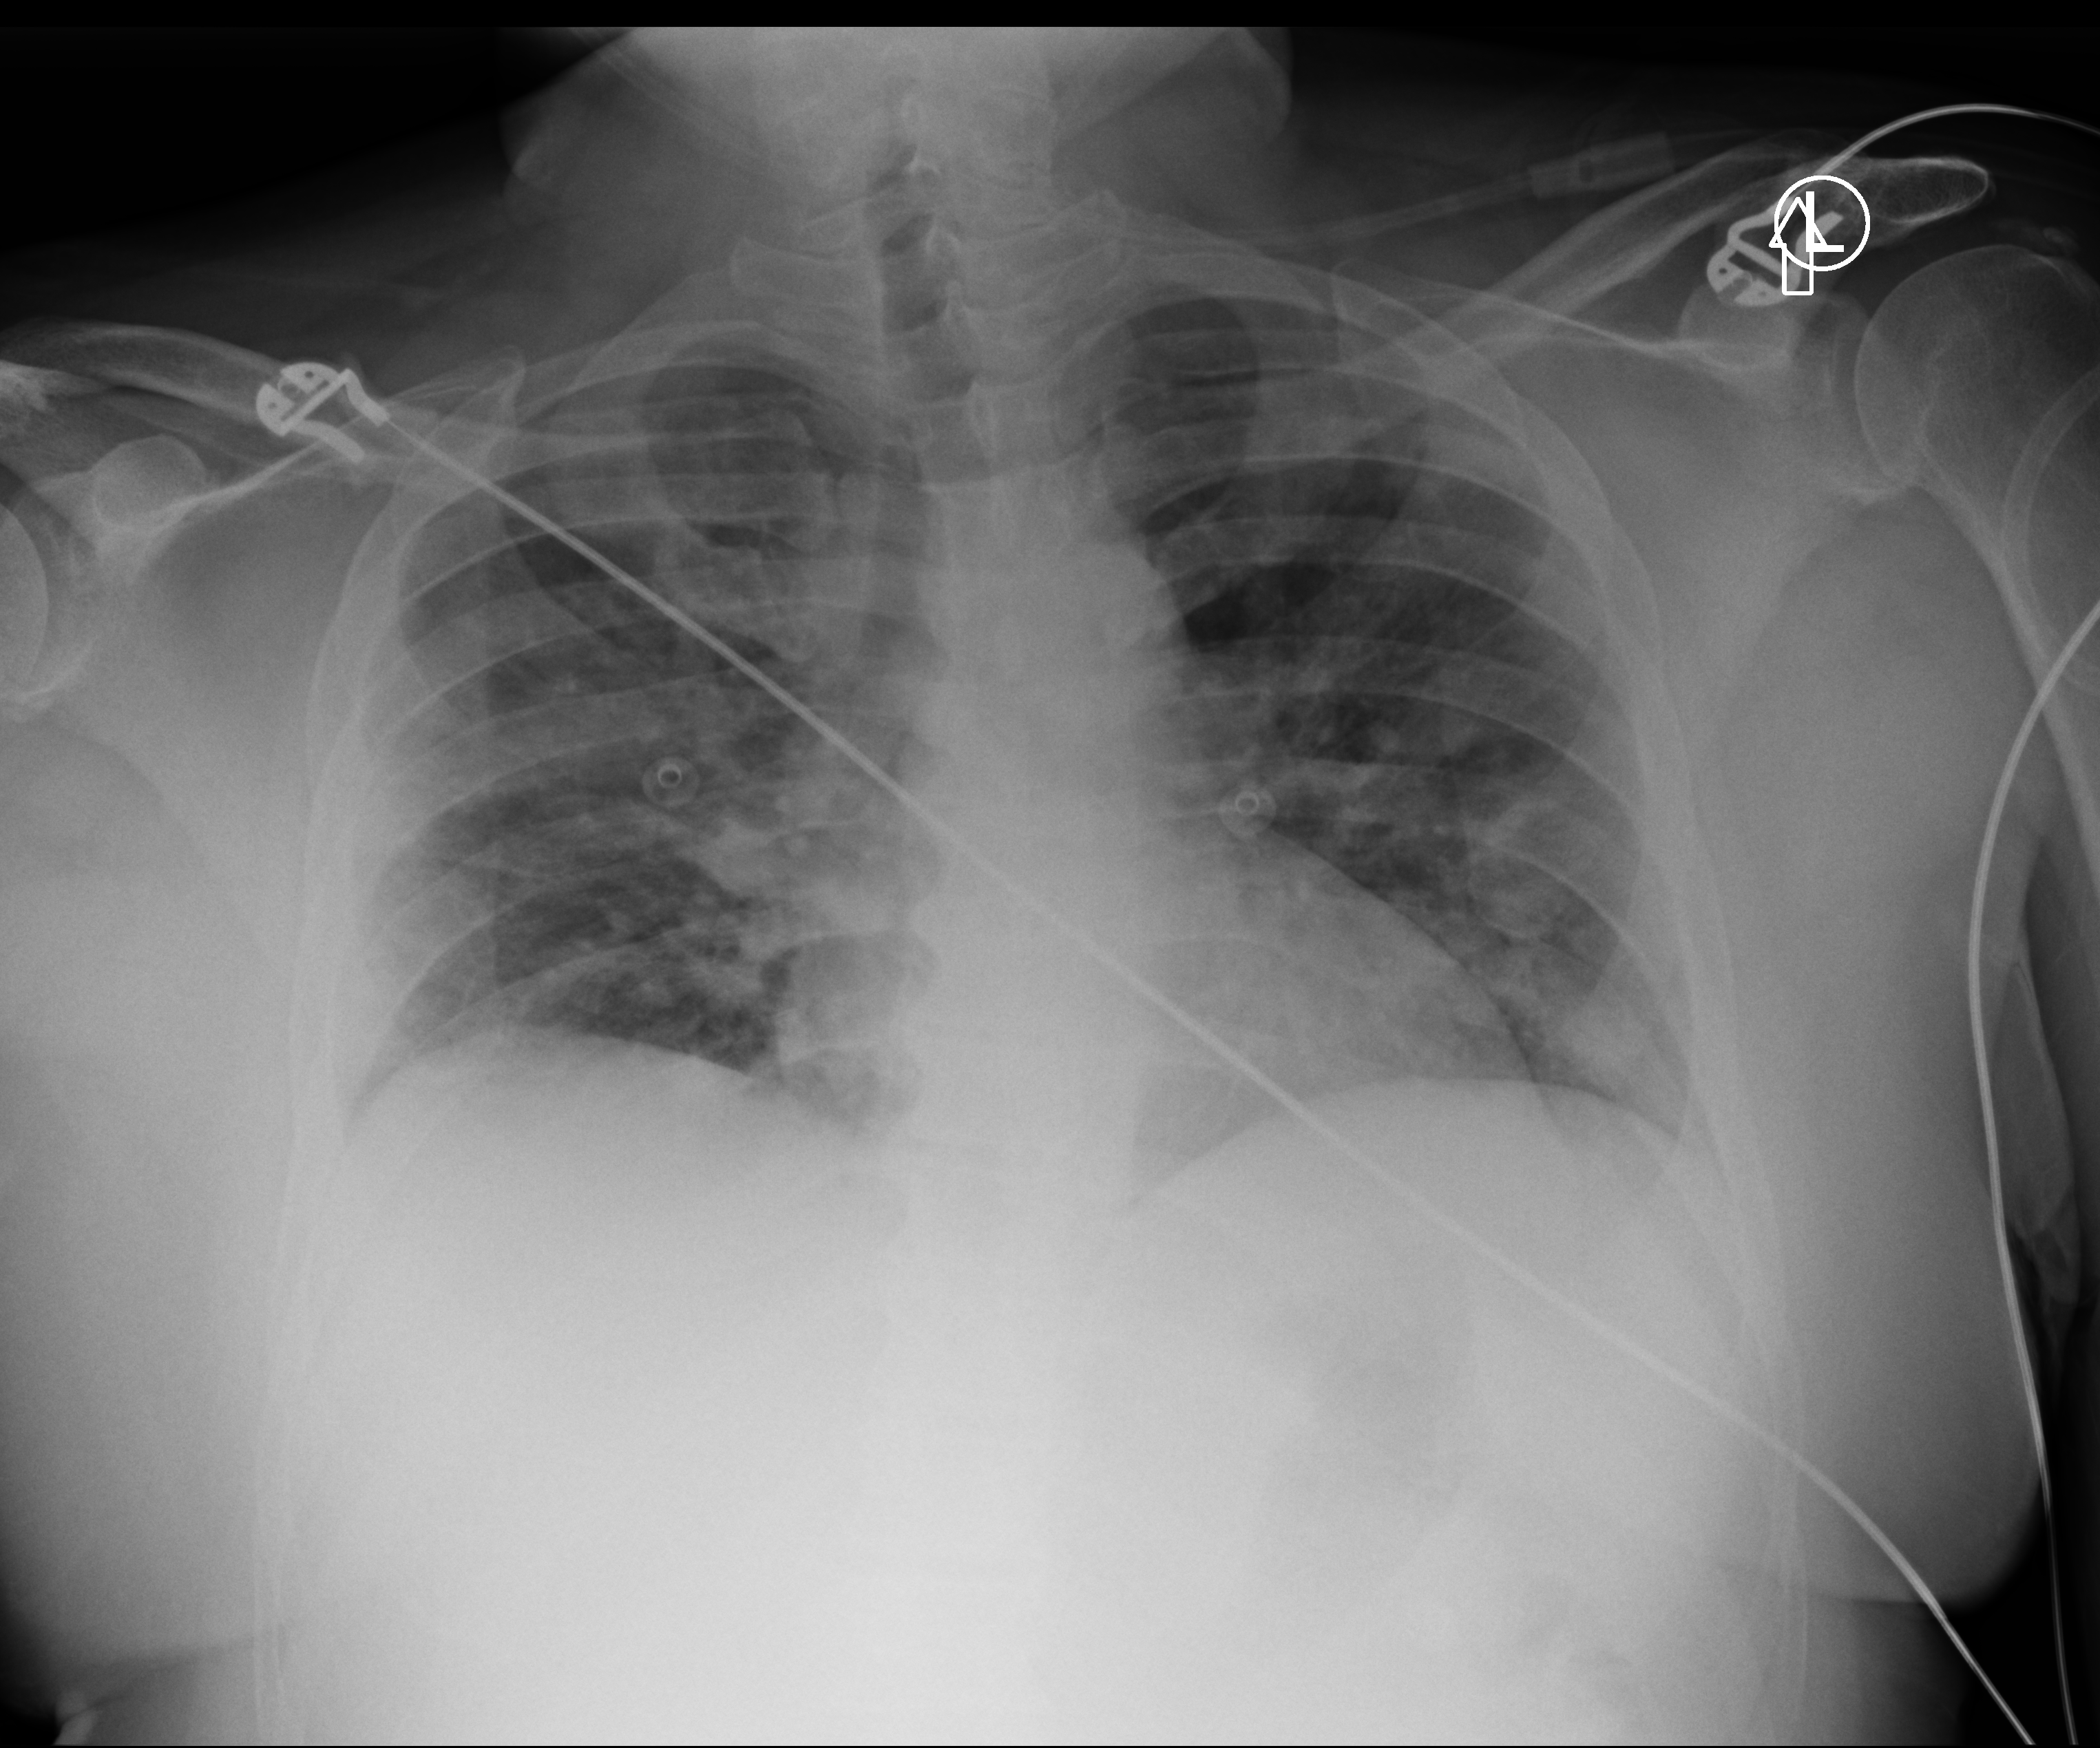
Chest X-ray (portable), anteroposterior (AP) projection. Patient hospitalised with COVID-19; male, aged 60–74 years.
Admission-level facts for this patient (not findings on this image; timing relative to this image not recorded):
- admitted to intensive care during this hospital stay: no